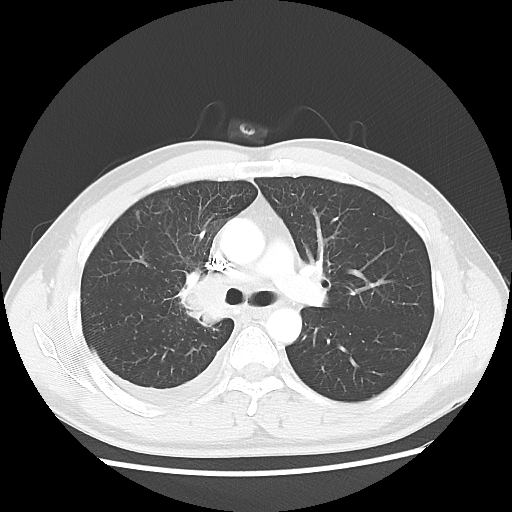
Chest CT, one axial slice. Position 34 of 56 along the scan axis. Reconstruction kernel LUNG. 120 kVp. Lung window (W 1500 / L -600 HU). 5 mm slice thickness. 512 × 512 image matrix, field of view 360 × 360 mm. Patient: male, 46 years. Case-level facts recorded for this patient, not image findings: clinical TNM (as recorded): T2 N3 M1.
Annotated regions visible in this slice (bounding box drawn by a radiologist):
- lung tumour (recorded histology: adenocarcinoma): box from (x=176, y=265) to (x=231, y=340) px